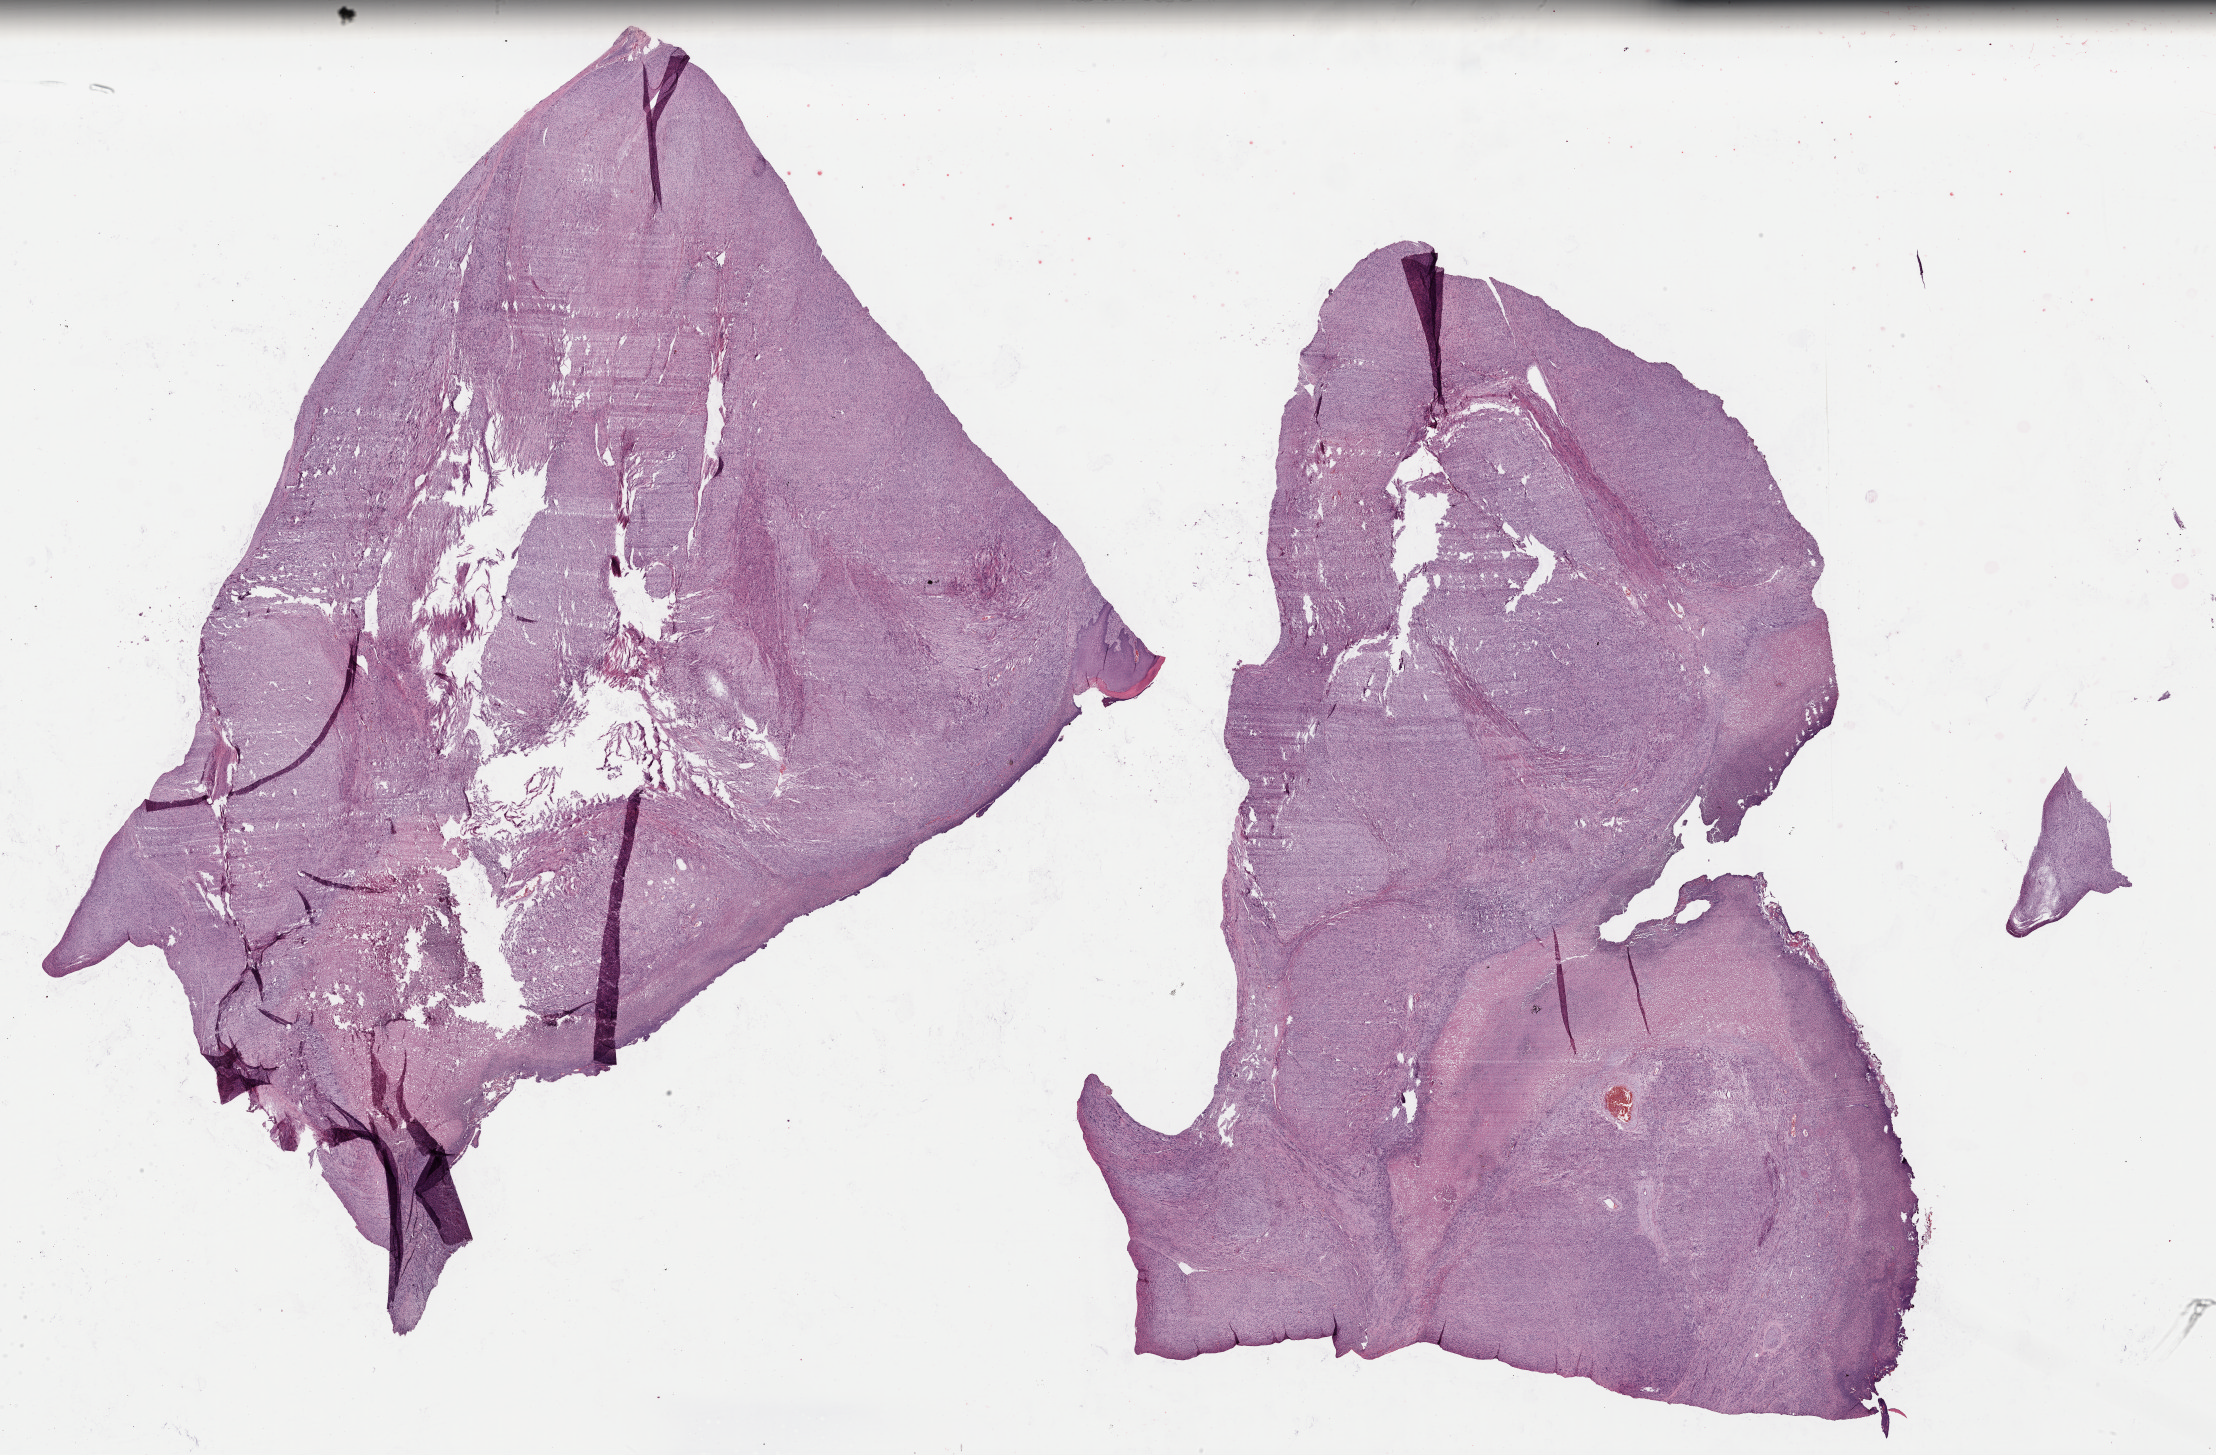
Whole-slide histology image, Hematoxylin and eosin (H&E) stained, a low-resolution overview of the entire scanned area, about 35.0 x 23.0 mm (from a 40x scan); formalin-fixed paraffin-embedded (FFPE) diagnostic section; primary tumour sample from the retroperitoneum and peritoneum. Patient: female, age at initial diagnosis 57 years.
Histologic diagnosis: Leiomyosarcoma, NOS (retroperitoneum).